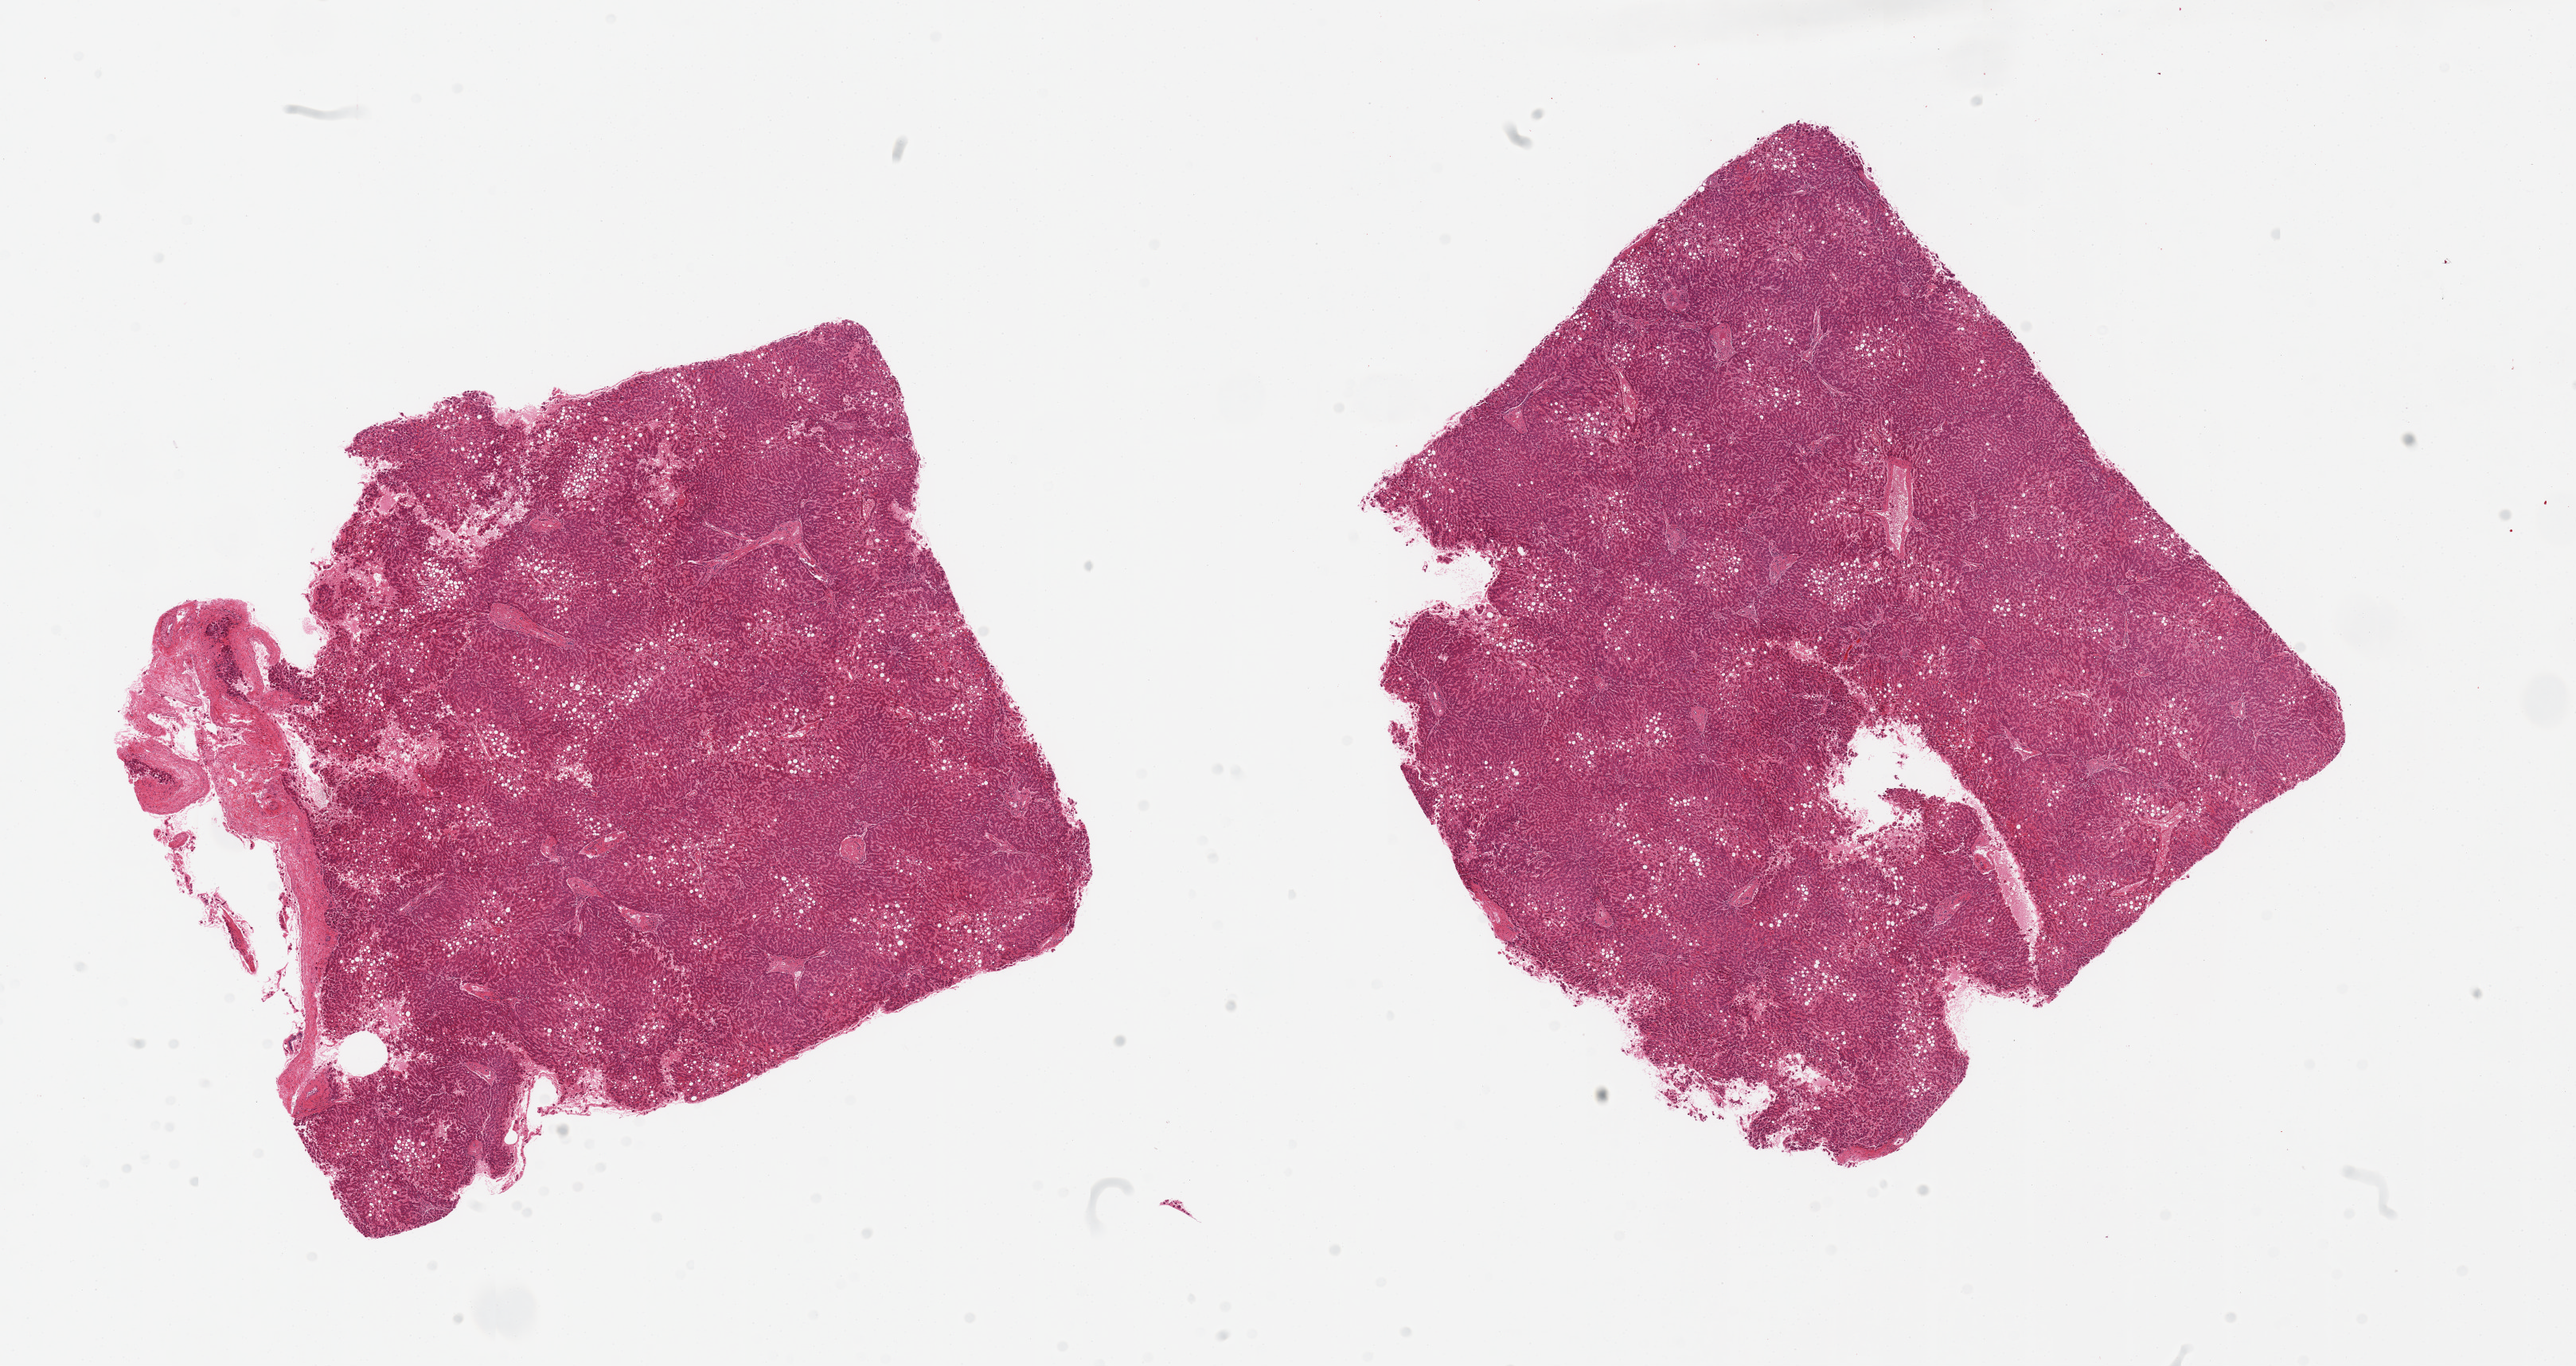
Whole-slide image, haematoxylin and eosin stain, a low-resolution overview of the entire scanned area, about 25.6 x 13.6 mm (from a 20x scan). PAXgene-fixed, paraffin-embedded tissue. Sampled site (target tissue): liver. Donor tissue sample. Male donor.
Reviewer comment on this tissue sample: 2 pieces, moderate passive congestion; ~15-20% macrovesicular steatosis.